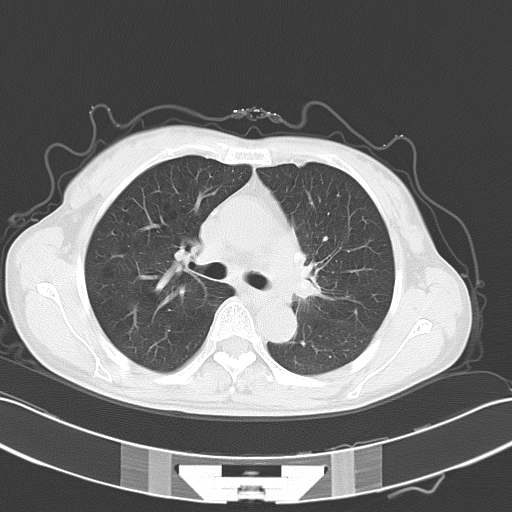
Chest CT, one axial slice; slice 36 of 54 in the series (ordered by position); reconstruction kernel B70f; lung window (W 1500 / L -600 HU); 5 mm slice thickness; 512 × 512 image matrix, field of view 353 × 353 mm. Female patient, age 50 years. Case-level facts recorded for this patient, not image findings: clinical TNM (as recorded): T2a N1 M1c.
Annotated regions visible in this slice (rectangle marked by the reading radiologist):
- lung tumour (recorded histology: adenocarcinoma): box from (x=299, y=245) to (x=320, y=303) px